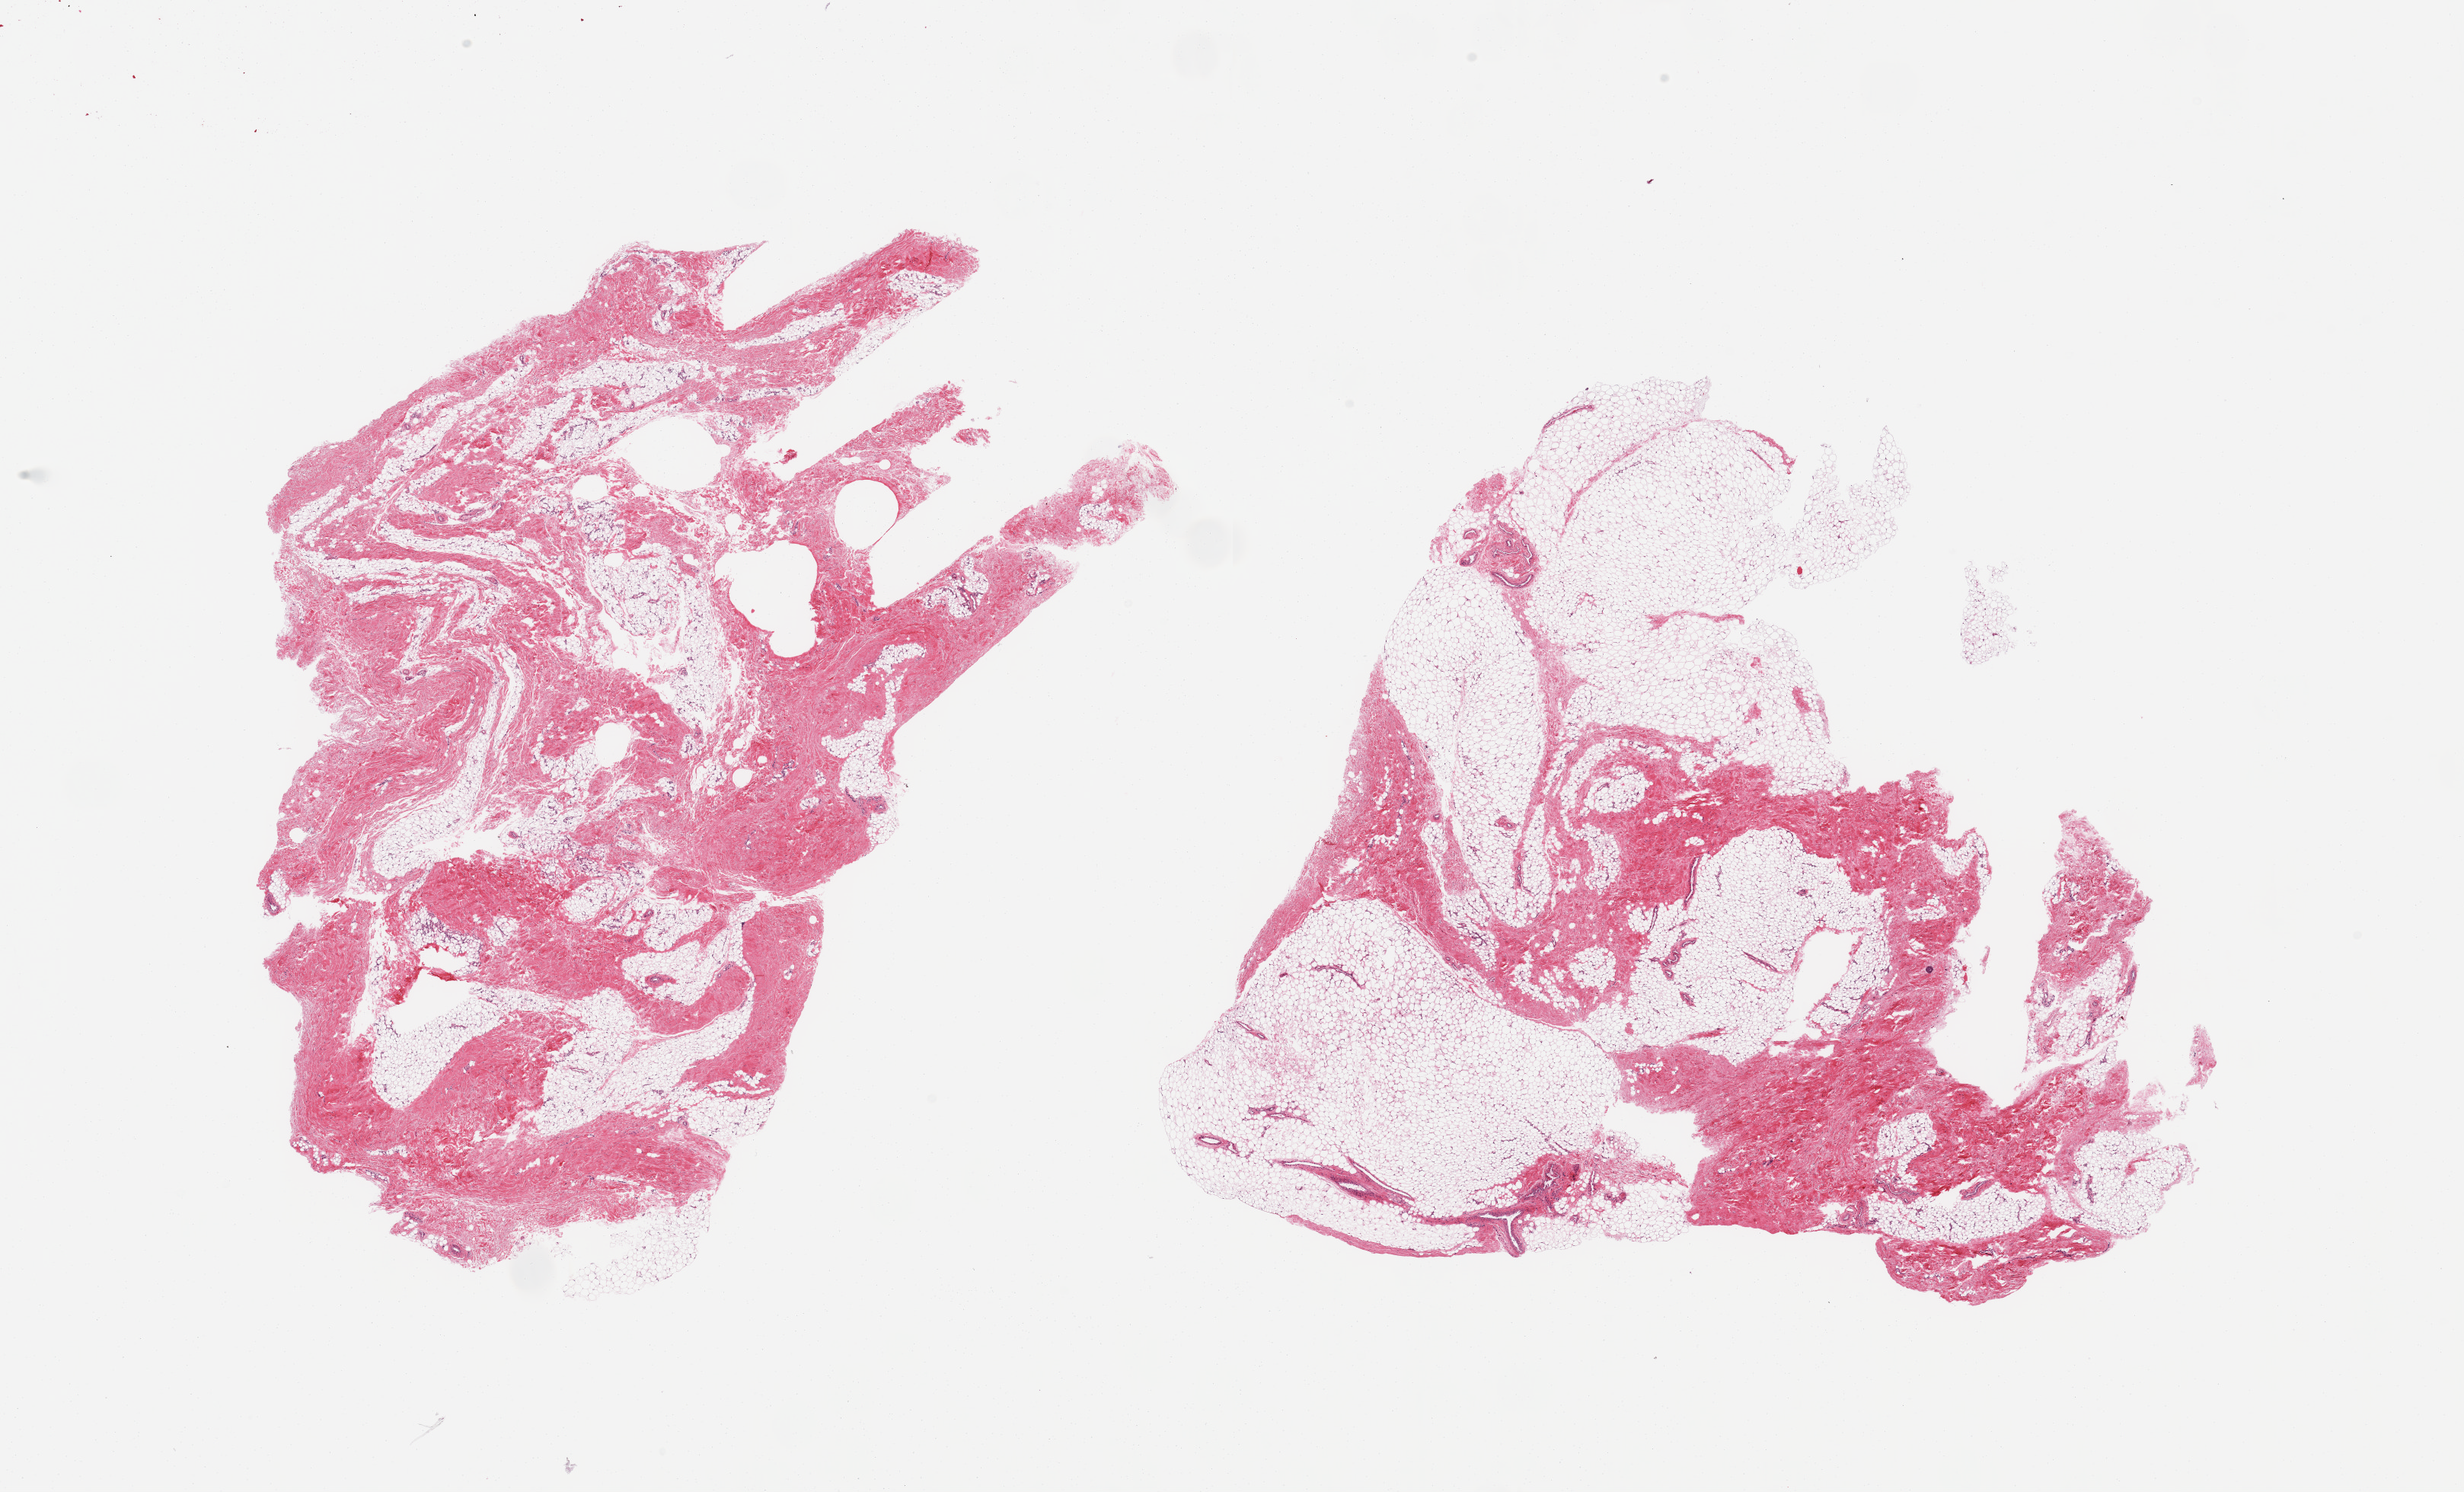
Digitized haematoxylin and eosin-stained section, a low-resolution overview of the entire scanned area, about 25.6 x 15.5 mm; PAXgene-fixed, paraffin-embedded tissue; sampled site (target tissue): breast; tissue donor sample. Donor: male.
- review note (as recorded): 2 pieces, fibroadipose elements; Minute incidental soft tissue calcospherule noted